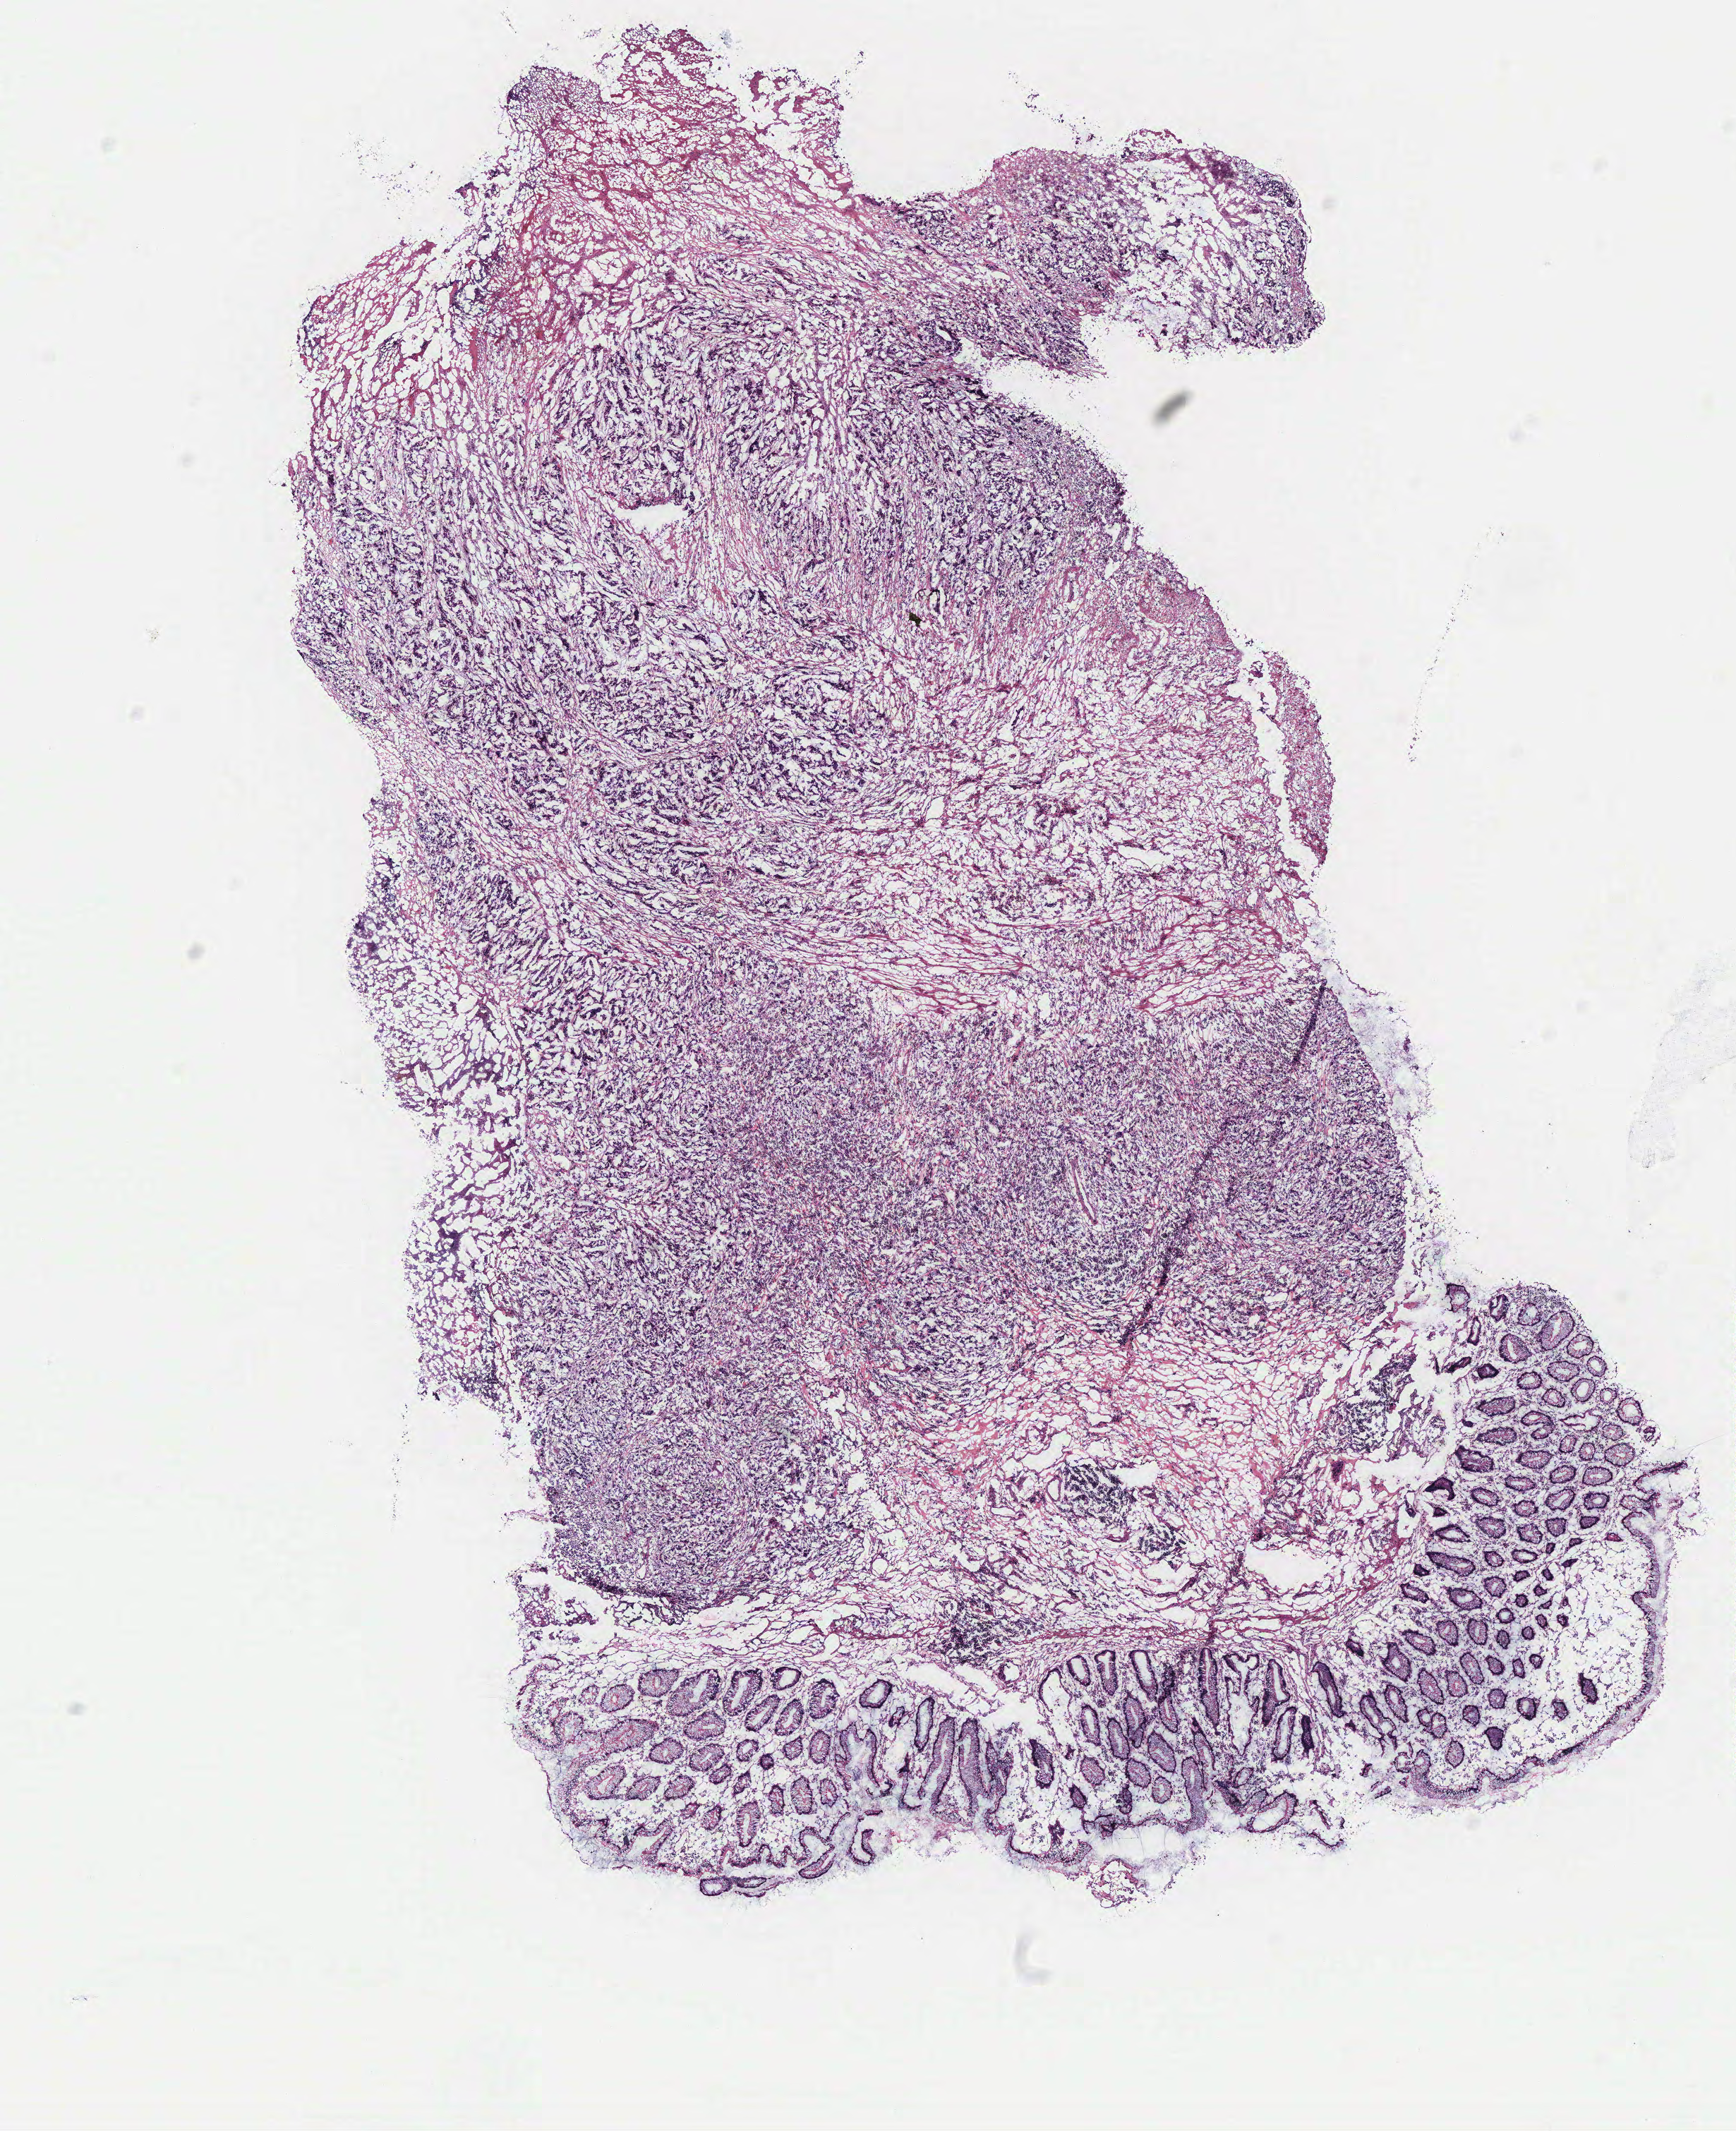
Digitized Hematoxylin and eosin (H&E) stained tissue section (whole slide) — shown as a low-resolution overview of the whole scanned area (about 9.8 x 12.1 mm, acquisition: 40x scan). Colon, normal (non-tumour) tissue. 73-year-old female patient.
This section: normal (non-tumour) tissue from the same patient. Patient diagnosis: Adenocarcinoma, NOS.